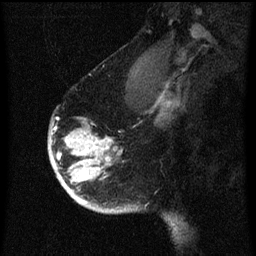
Breast MRI (dynamic contrast-enhanced), one sagittal slice. Slice 47 of 60 in the series (ordered by position). Dynamic contrast-enhanced series, image 2 of 3 at this slice position (ordered by acquisition). 1.5 T. TE 4.2 ms, TR 8 ms. 2 mm slice thickness. 256 × 256 image matrix, field of view 180 × 180 mm. Patient: female, 56 years.
Structures marked on this image (semi-automatic segmentation, software-assisted and operator-edited):
- analysis volume of interest (the breast-tissue region the enhancement analysis was run in; not a lesion): bounding box (x1, y1, x2, y2) in pixels: (50, 108, 125, 215)
- tumour enhancement mask (voxels above the 70 % enhancement threshold inside the analysis volume of interest): (50, 130, 121, 213)